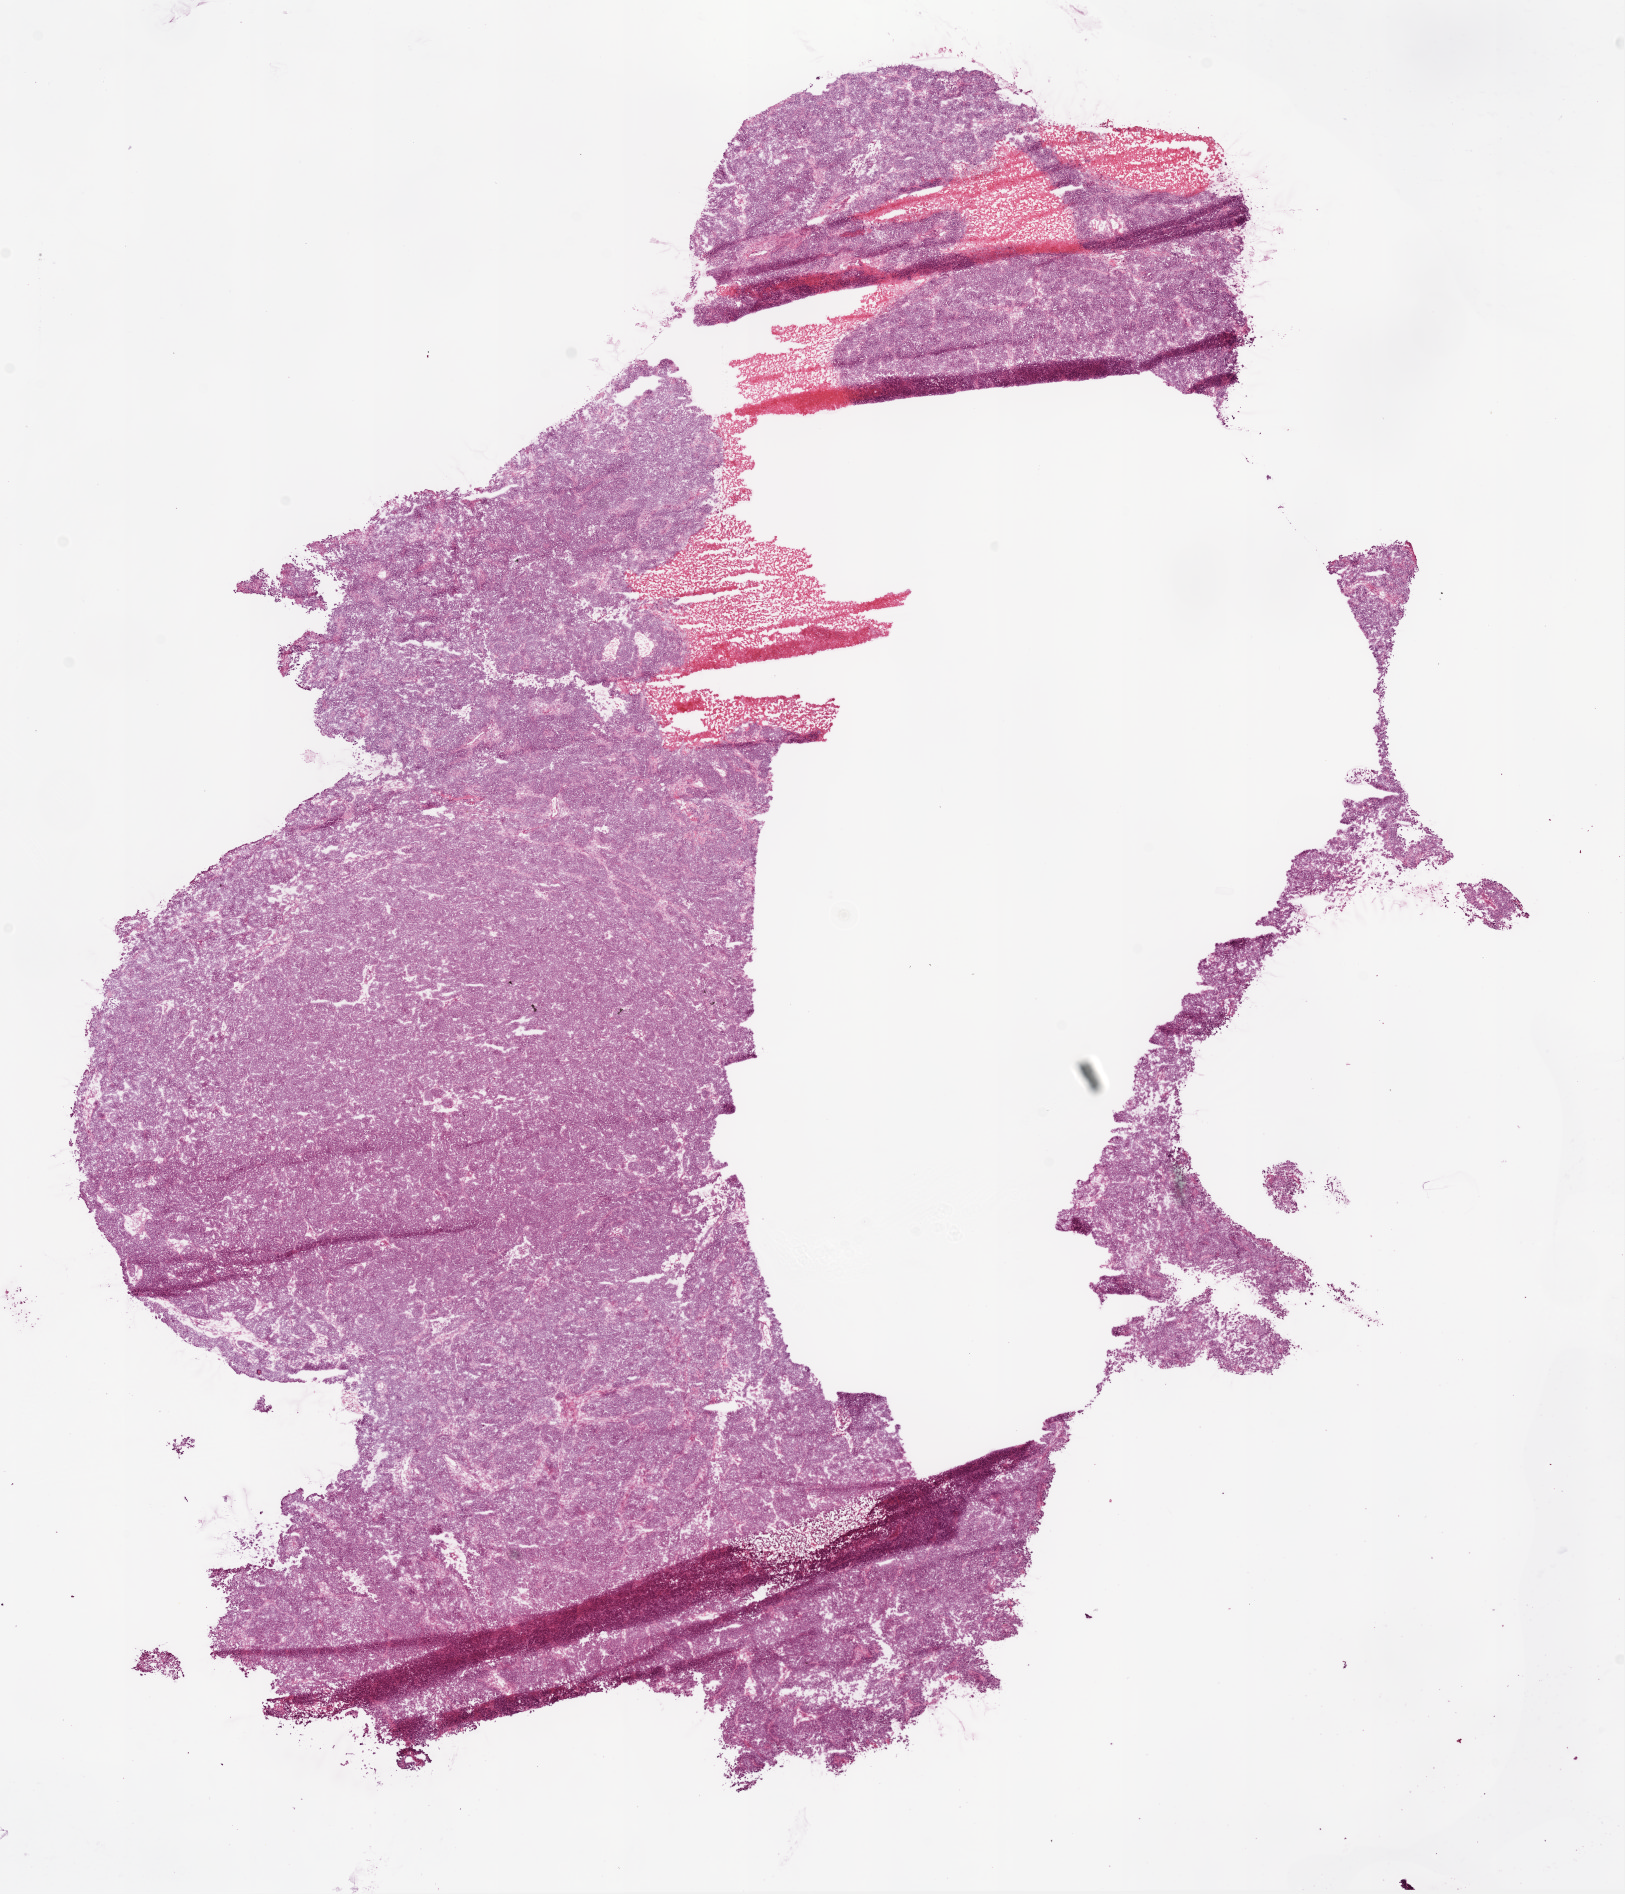
Digitized H&E-stained tissue section (whole slide), a low-resolution overview of the entire scanned area, about 13.0 x 15.2 mm; frozen section; ovary, recurrent tumour sample. Patient: female, age at initial diagnosis 40 years. Slide review estimates, as recorded: tumour cells 75%, tumour nuclei 85%.
This section: recurrent tumour. Patient diagnosis: Serous cystadenocarcinoma, NOS.